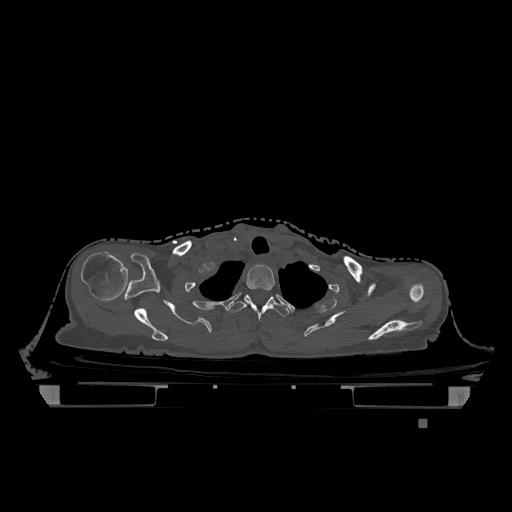
CT including the spine, one axial slice; position 979 of 1317 along the scan axis; bone window (W 1800 / L 400 HU); 512 × 512 image matrix. Female patient, age 74 years. Case-level facts recorded for this patient, not image findings: primary cancer: lung; vertebrae with lytic lesions (as recorded): T1, T4, T5, T6, L4, L5.
Annotated regions visible in this slice (semi-automatically segmented with operator editing):
- T1 vertebra: bounding box (x1, y1, x2, y2) in pixels: (246, 264, 275, 291)
- T2 vertebra: (227, 295, 290, 321)